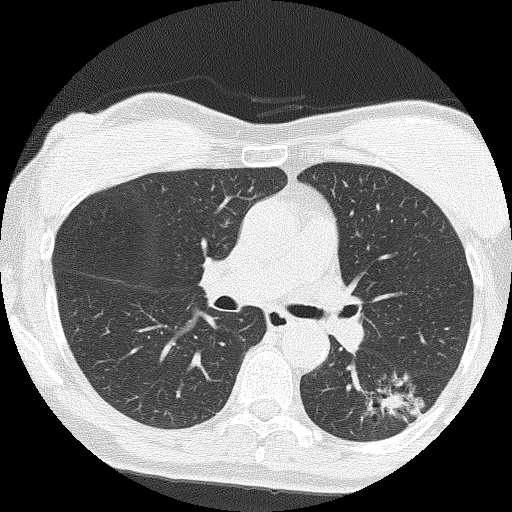
Low-dose screening chest CT, axial slice, second screening round (one year after baseline), lung window (W 1500 / L -600 HU), 2 mm slice thickness, 512 × 512 image matrix. Female participant, aged 64 years at enrolment. Former smoker at enrolment.
• Expert reader's lesion annotation, box from (x=357, y=373) to (x=434, y=438) px.
• The screening reader recorded 3 non-calcified nodules or masses ≥4 mm on this exam; which of them this box marks is not recorded.
• Official screen result: positive, other.
• Lung cancer was diagnosed 576 days after this screen: adenocarcinoma, NOS, left lower lobe, moderately differentiated (G2), stage IA (AJCC 6th edition), 17 mm at pathology.